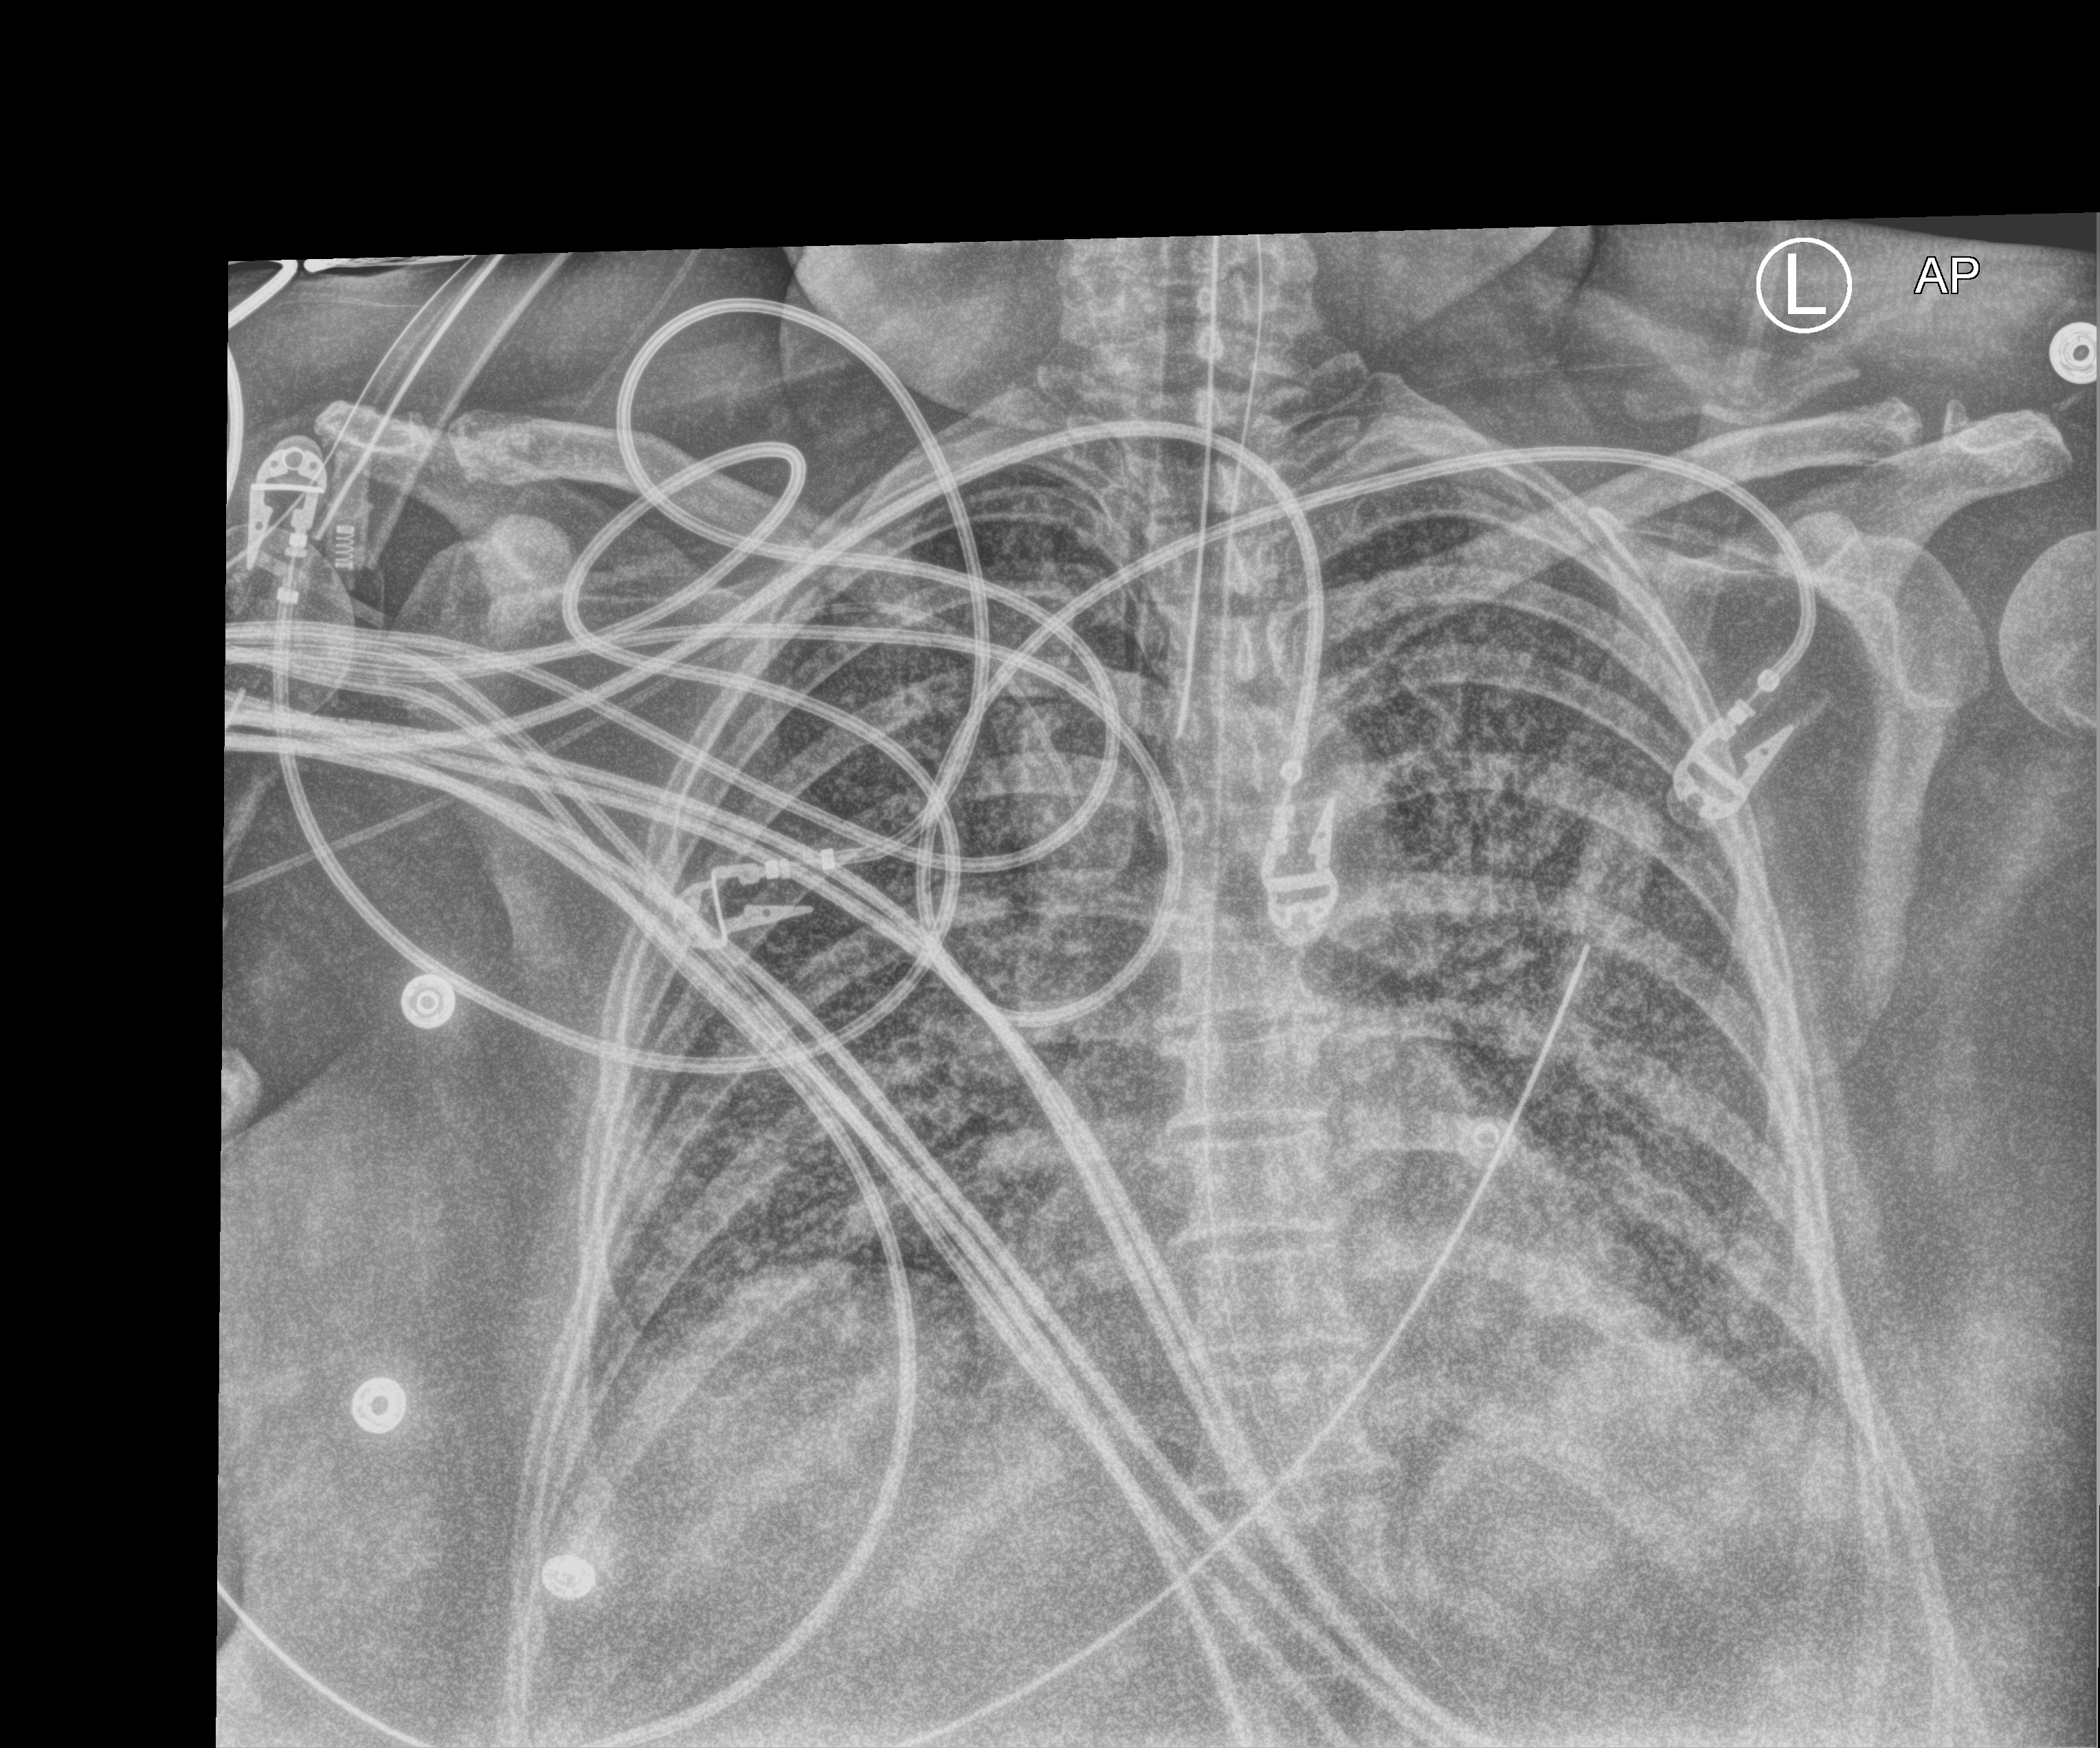
Bedside chest radiograph (computed radiography), anteroposterior (AP) projection. Patient hospitalised with COVID-19; female, aged 18–59 years.
Hospital-stay facts (about this admission, not read from this image; timing relative to this image not recorded): length of hospital stay: 95 days; mechanically ventilated during this hospital stay: yes; other chronic lung disease (admission record): no.